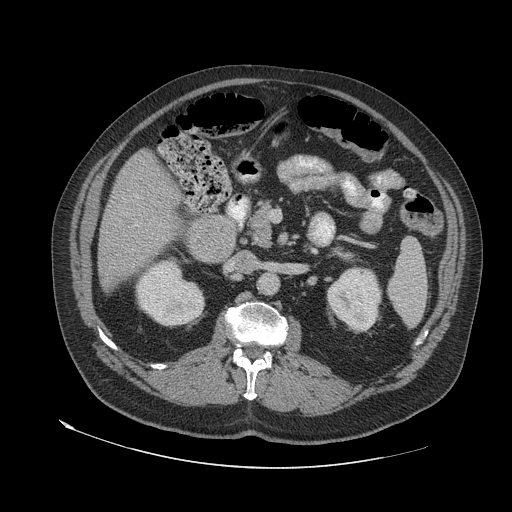
Contrast-enhanced abdominal CT (liver protocol), one axial slice; slice 22 of 79 in the series (ordered by position); reconstruction kernel STANDARD; soft-tissue window (W 400 / L 40 HU); 512 × 512 image matrix, field of view 480 × 480 mm. Case-level facts recorded for this patient, not image findings: diagnosis: hepatocellular carcinoma (patient treated with transarterial chemoembolisation; whether this scan precedes or follows treatment is not stated here); TNM stage (as recorded): Stage-IVA; Child-Pugh class: A; tumour differentiation: well differentiated.
Outlined on this slice (semi-automatically segmented with operator editing):
- liver parenchyma outside the tumour (the mass and vessels are separate outlines, so this box may not span the whole liver): bounding box <98,150,180,290> (left, top, right, bottom; pixels)